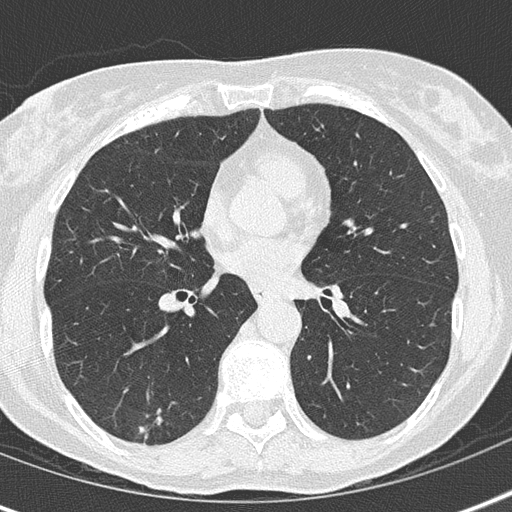
Chest CT (low-dose screening protocol), one axial image; first (baseline) screen; lung window (W 1500 / L -600 HU); lung (sharp) reconstruction kernel (B50f). Female, age 69 years at enrolment.
• Expert reader's lesion annotation, bounding box <116,400,180,457> (left, top, right, bottom; pixels).
• The screening reader recorded 2 non-calcified nodules or masses ≥4 mm on this exam (right lower lobe, left lower lobe); which of them this box marks is not recorded.
• Lung cancer was diagnosed 476 days after this screen: adenocarcinoma, NOS, right lower lobe, moderately differentiated (G2), stage IA (AJCC 6th edition), 16 mm at pathology.